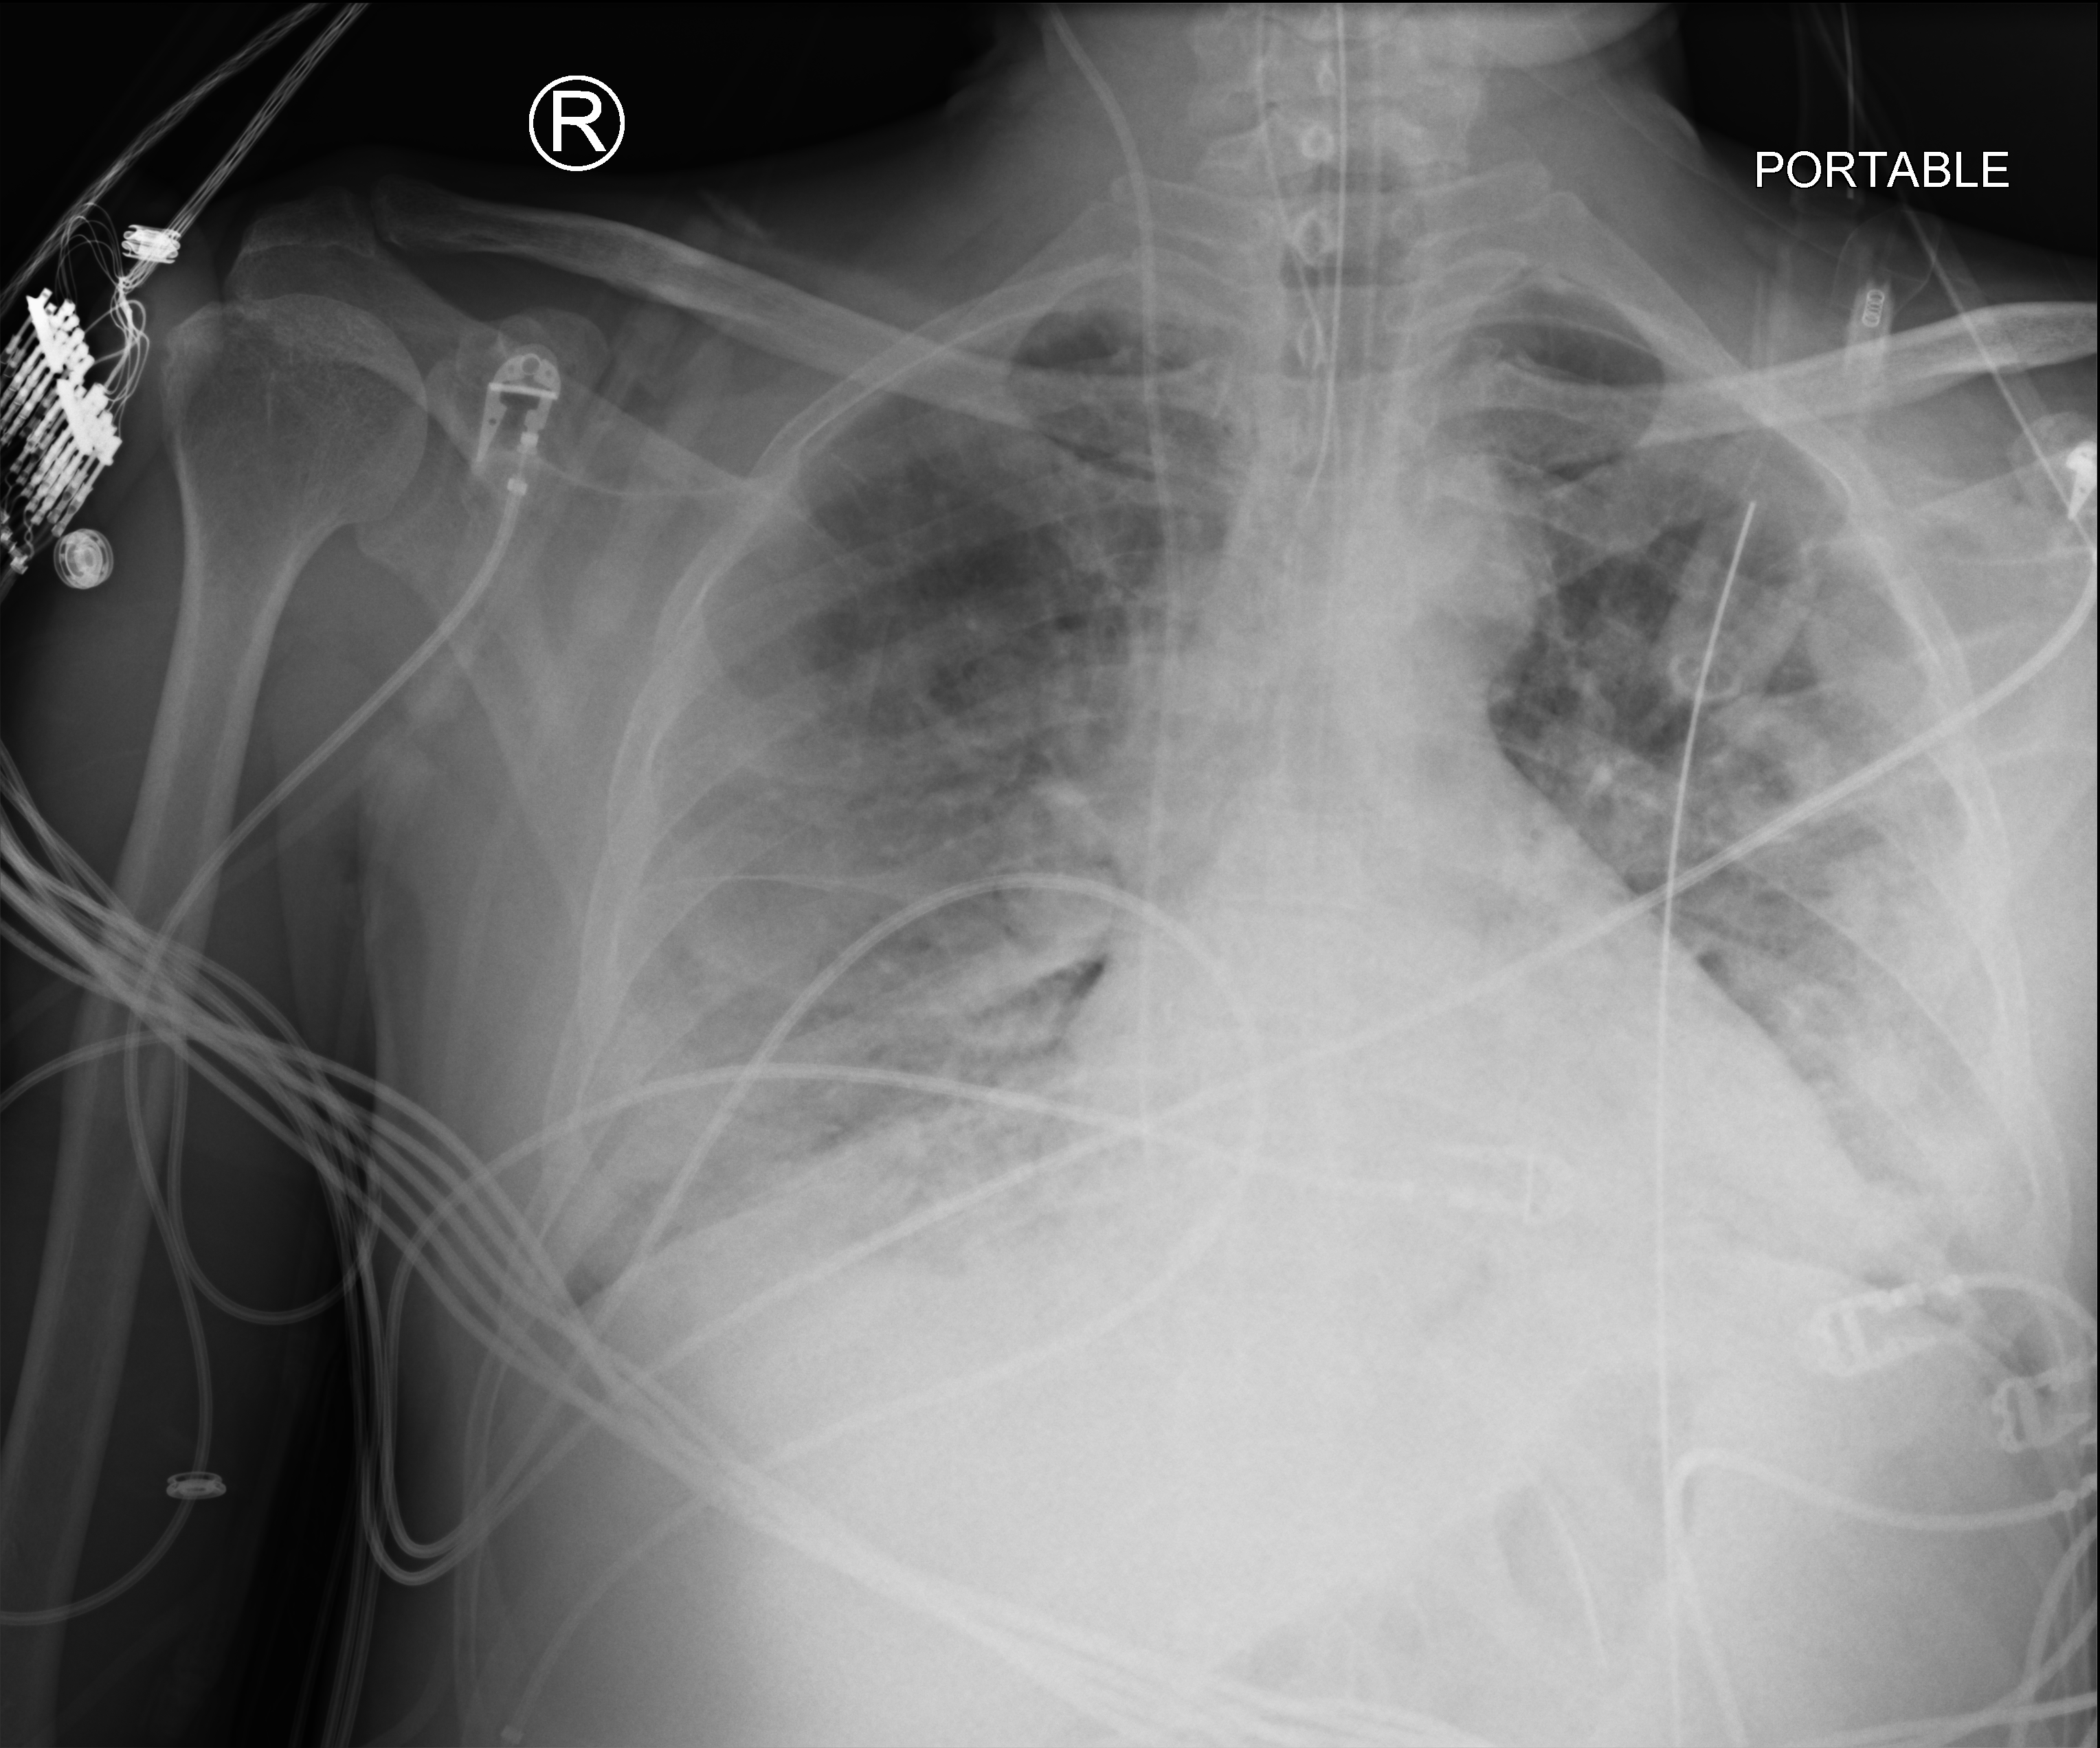
Chest X-ray (portable); anteroposterior (AP) projection. Patient hospitalised with COVID-19; male, aged 18–59 years.
From the hospital-stay record, not from the radiograph (when in the stay this image was taken is not recorded): length of hospital stay: 41 days; chronic kidney disease (admission record): no; mechanically ventilated during this hospital stay: yes.